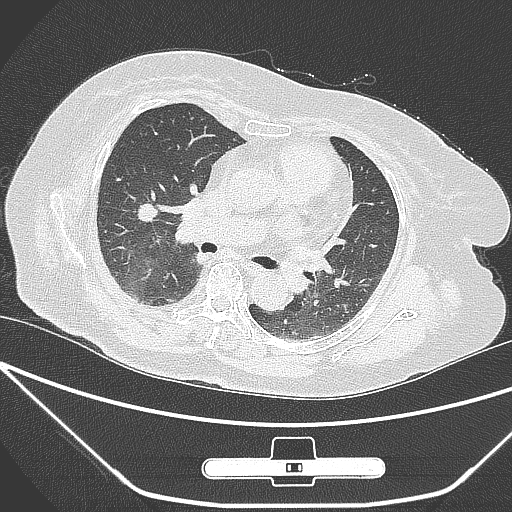
Chest CT, one axial slice; slice 155 of 245 in the series (ordered by position); lung window (W 1500 / L -600 HU); 1 mm slice thickness; 512 × 512 image matrix. Patient: female, 65 years. Case-level facts recorded for this patient, not image findings: clinical TNM (as recorded): T1c N0 M0.
Structures marked on this image (bounding box drawn by a radiologist):
- lung tumour (recorded histology: adenocarcinoma): bounding box [x1, y1, x2, y2] px = [130, 194, 163, 234]